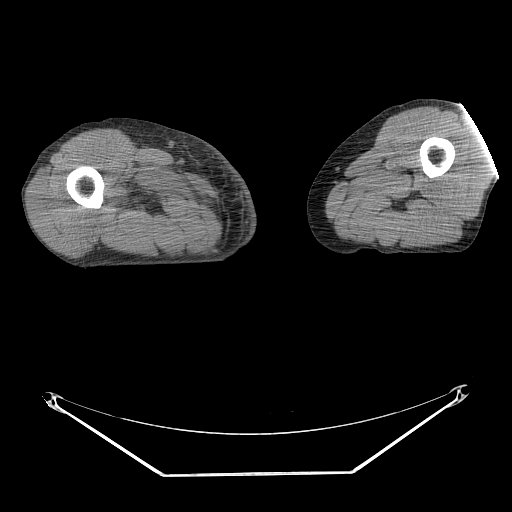
CT of an extremity soft-tissue mass (from a PET/CT study), one axial slice; position 230 of 311 along the scan axis; reconstruction kernel STANDARD; 140 kVp; soft-tissue window (W 400 / L 40 HU); 3.75 mm slice thickness; 512 × 512 image matrix. Male patient. Case-level facts recorded for this patient, not image findings: histological type: undifferentiated - pleiomorphic; grade: high; site of the primary tumour: right thigh.
Structures marked on this image (expert contour drawn on MRI and transferred to this co-registered scan by the dataset authors):
- gross tumour volume including surrounding oedema: bounding box (x1, y1, x2, y2) in pixels: (151, 205, 156, 211)